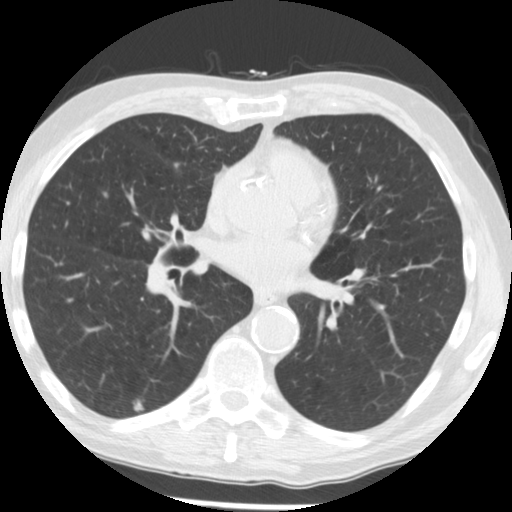
Axial slice from a low-dose chest CT screening exam. Second annual screen. Lung window (W 1500 / L -600 HU). 2.5 mm slice thickness. 512 × 512 image matrix, field of view 327 × 327 mm. Male participant, aged 62 years at enrolment.
• Expert-annotated lung lesion, bounding box [x1, y1, x2, y2] px = [121, 389, 158, 428].
• The screening reader recorded 2 non-calcified nodules or masses ≥4 mm on this exam; which of them this box marks is not recorded.